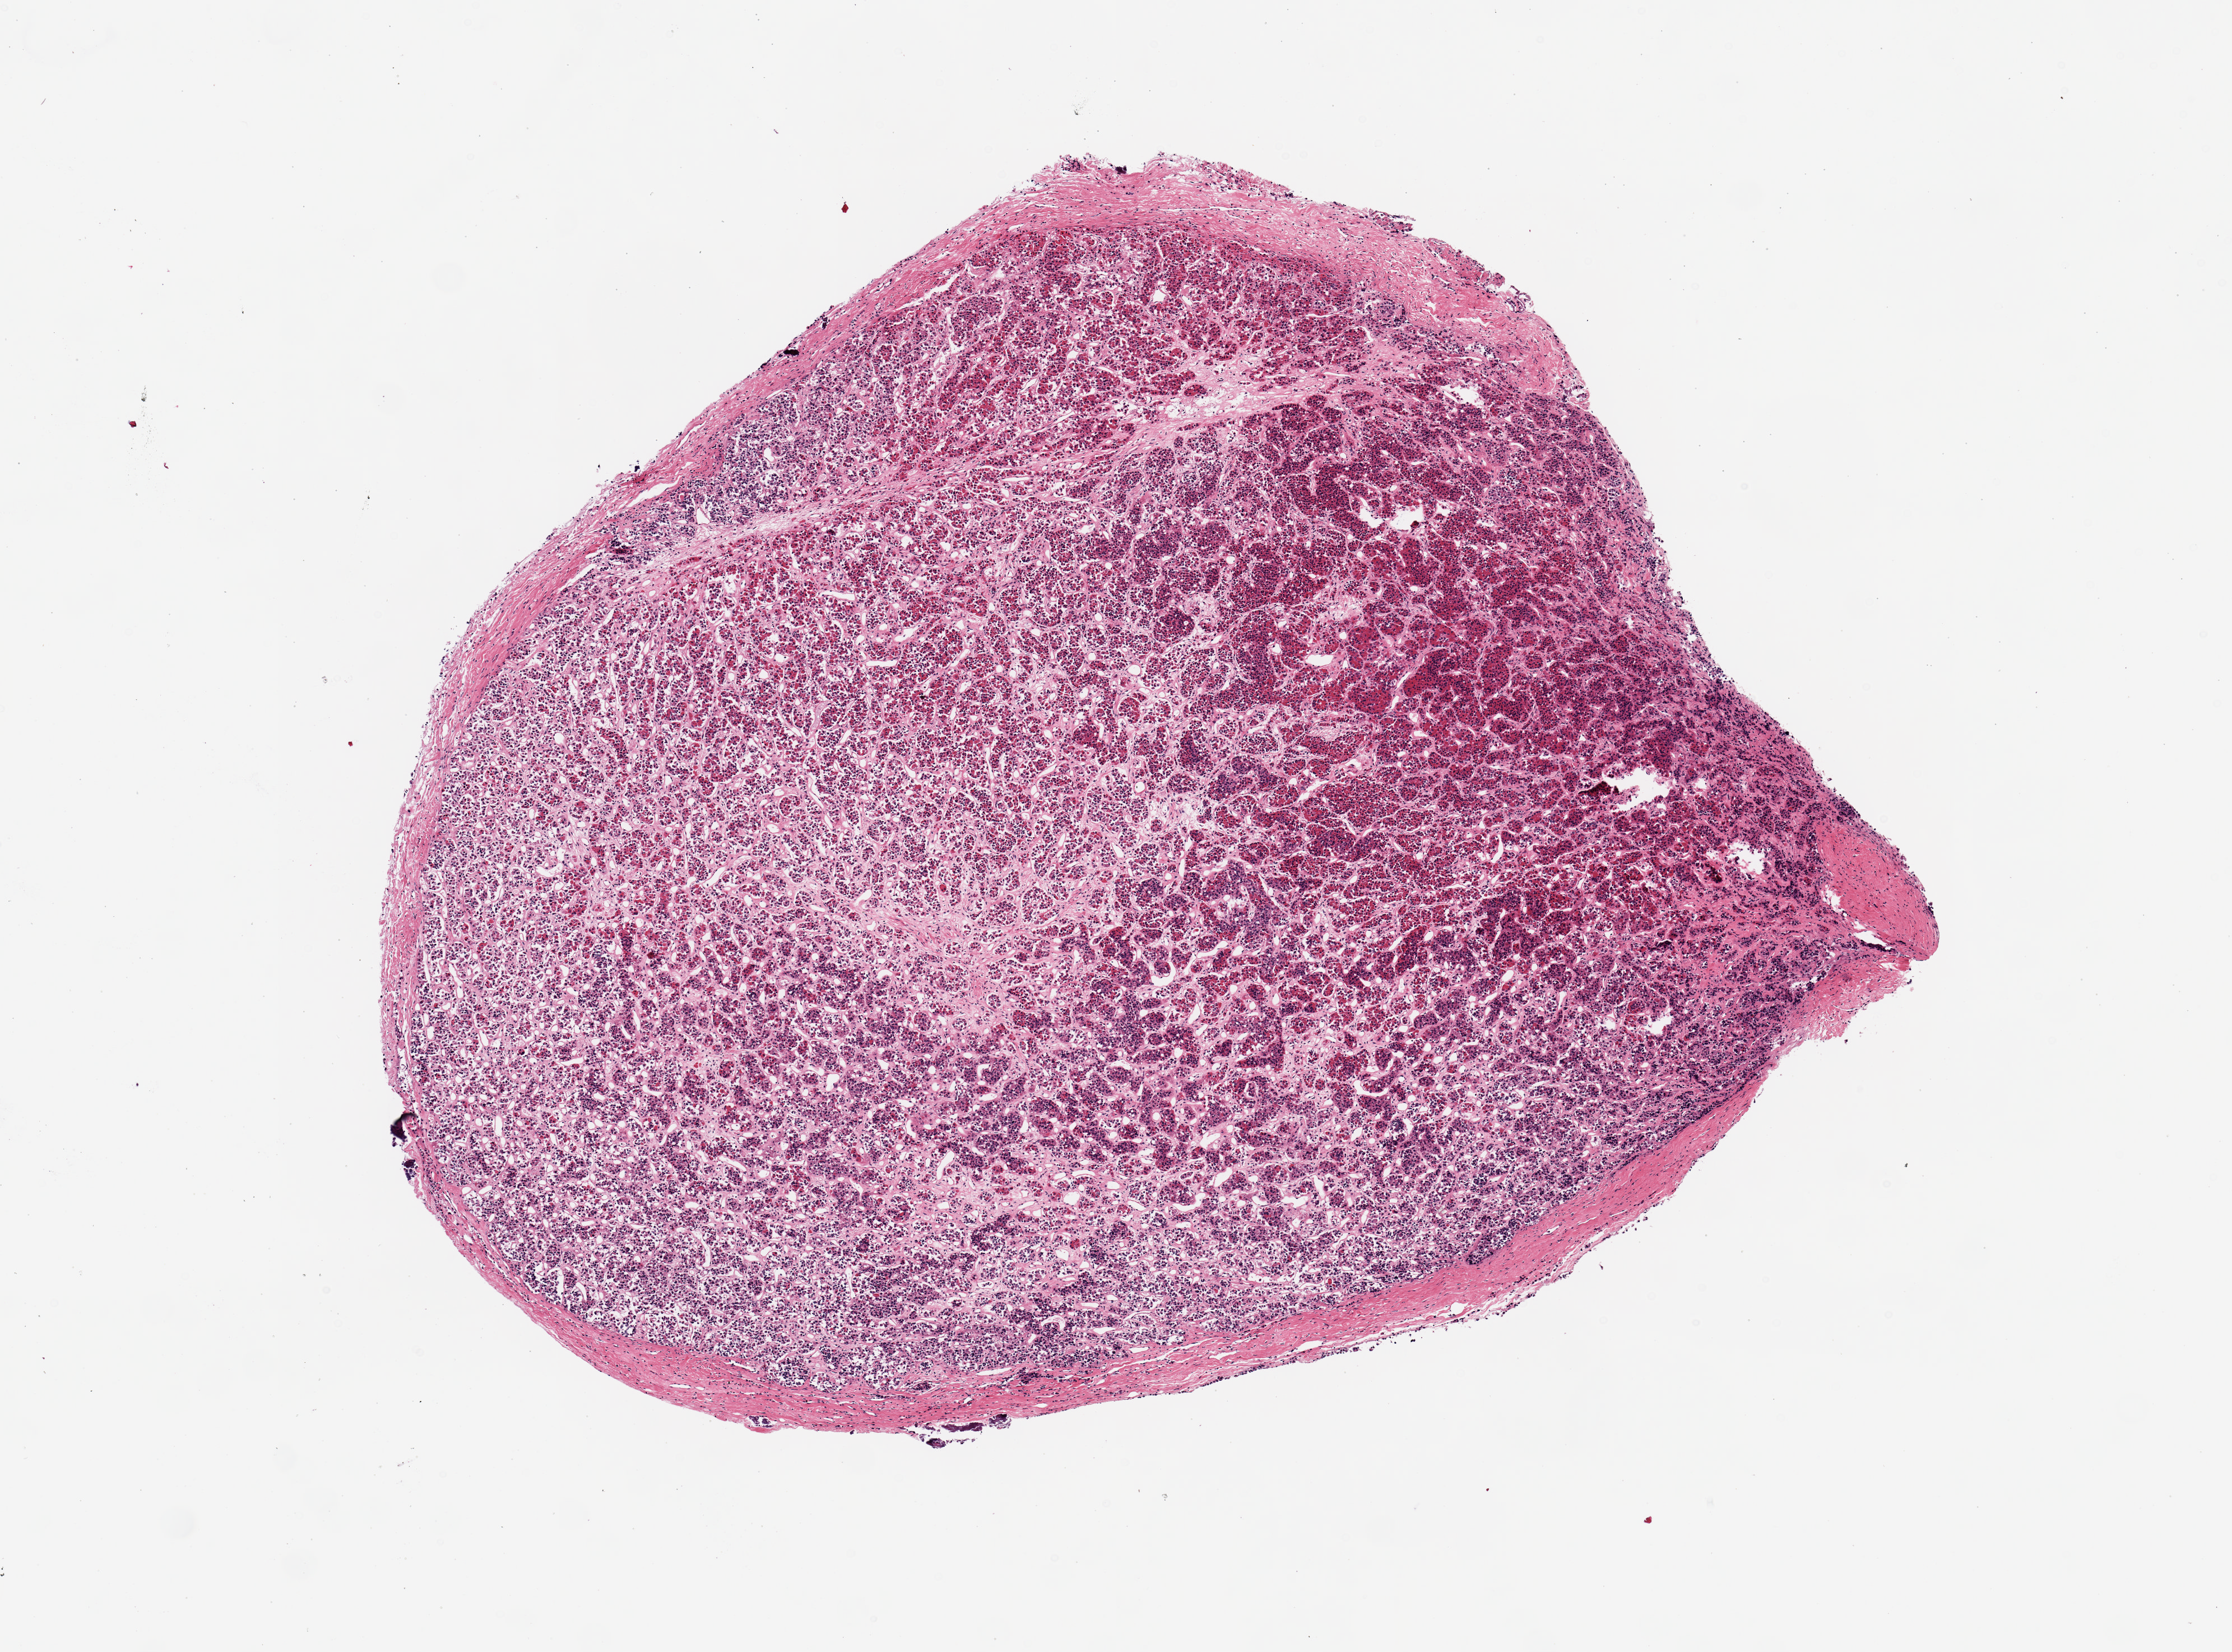
Hematoxylin and eosin (H&E) whole-slide image, low-resolution overview of the scanned area, about 7.9 x 5.8 mm; PAXgene-fixed paraffin-embedded (PFPE) section; sampled site (target tissue): pituitary; tissue donor sample. Donor sex: male.
Reviewer comment on this tissue sample: 1 ~ 5x4mm aliquot.